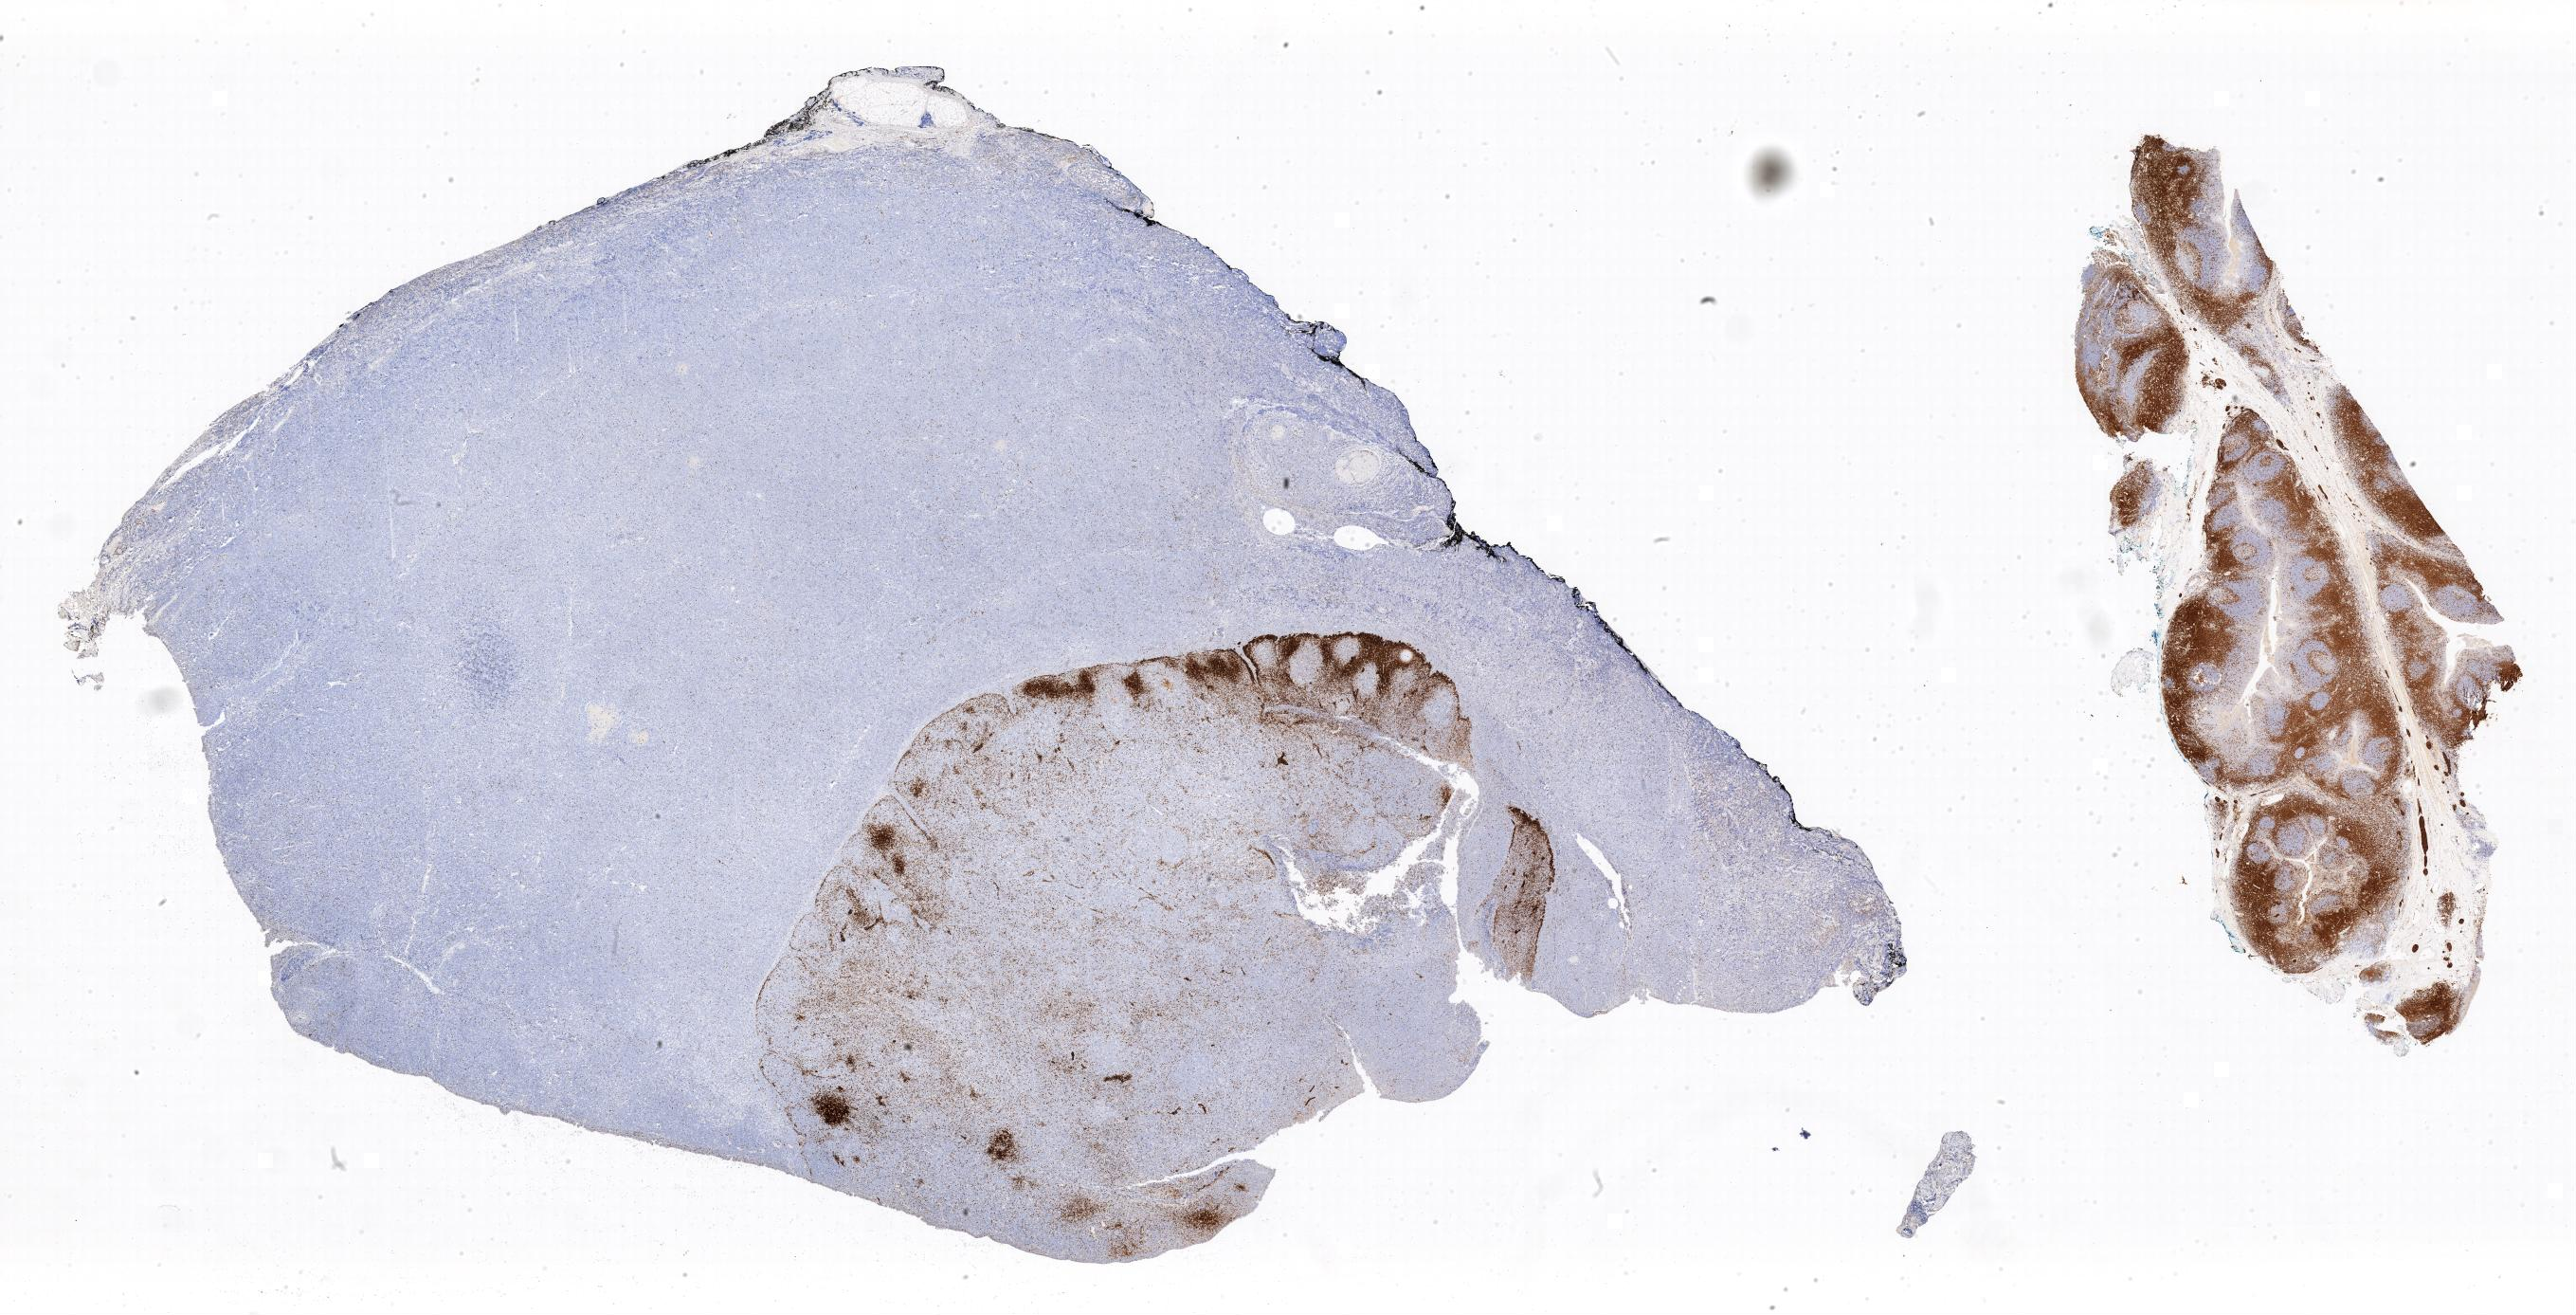
IHC for CD3, whole-slide image — whole scanned area shown as a low-resolution overview, tumor tissue, anatomic site: lymph node of head and neck. Male, age 6 years at initial diagnosis.
• diagnosis: Burkitt lymphoma, NOS